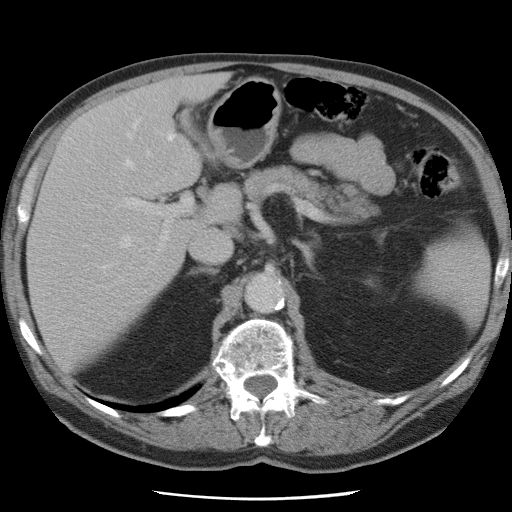
Contrast-enhanced abdominal CT, one axial slice; position 46 of 78 along the scan axis; 120 kVp; intravenous contrast given; soft-tissue window (W 400 / L 40 HU); 512 × 512 image matrix, field of view 337 × 337 mm. Male patient, age 75 years. From the clinical record (not read from this slice): diagnosis: colorectal cancer liver metastases, imaged before liver resection; multiple liver metastases: yes; largest metastasis: 2.4 cm; disease in both lobes: yes.
Annotated regions visible in this slice (manually delineated by an expert):
- hepatic veins: bounding box [x1, y1, x2, y2] px = [97, 120, 150, 274]
- liver: [28, 76, 240, 366]
- planned liver remnant (the part of the liver to remain after resection): [28, 121, 192, 368]
- portal vein (with intrahepatic branches): [123, 133, 193, 251]